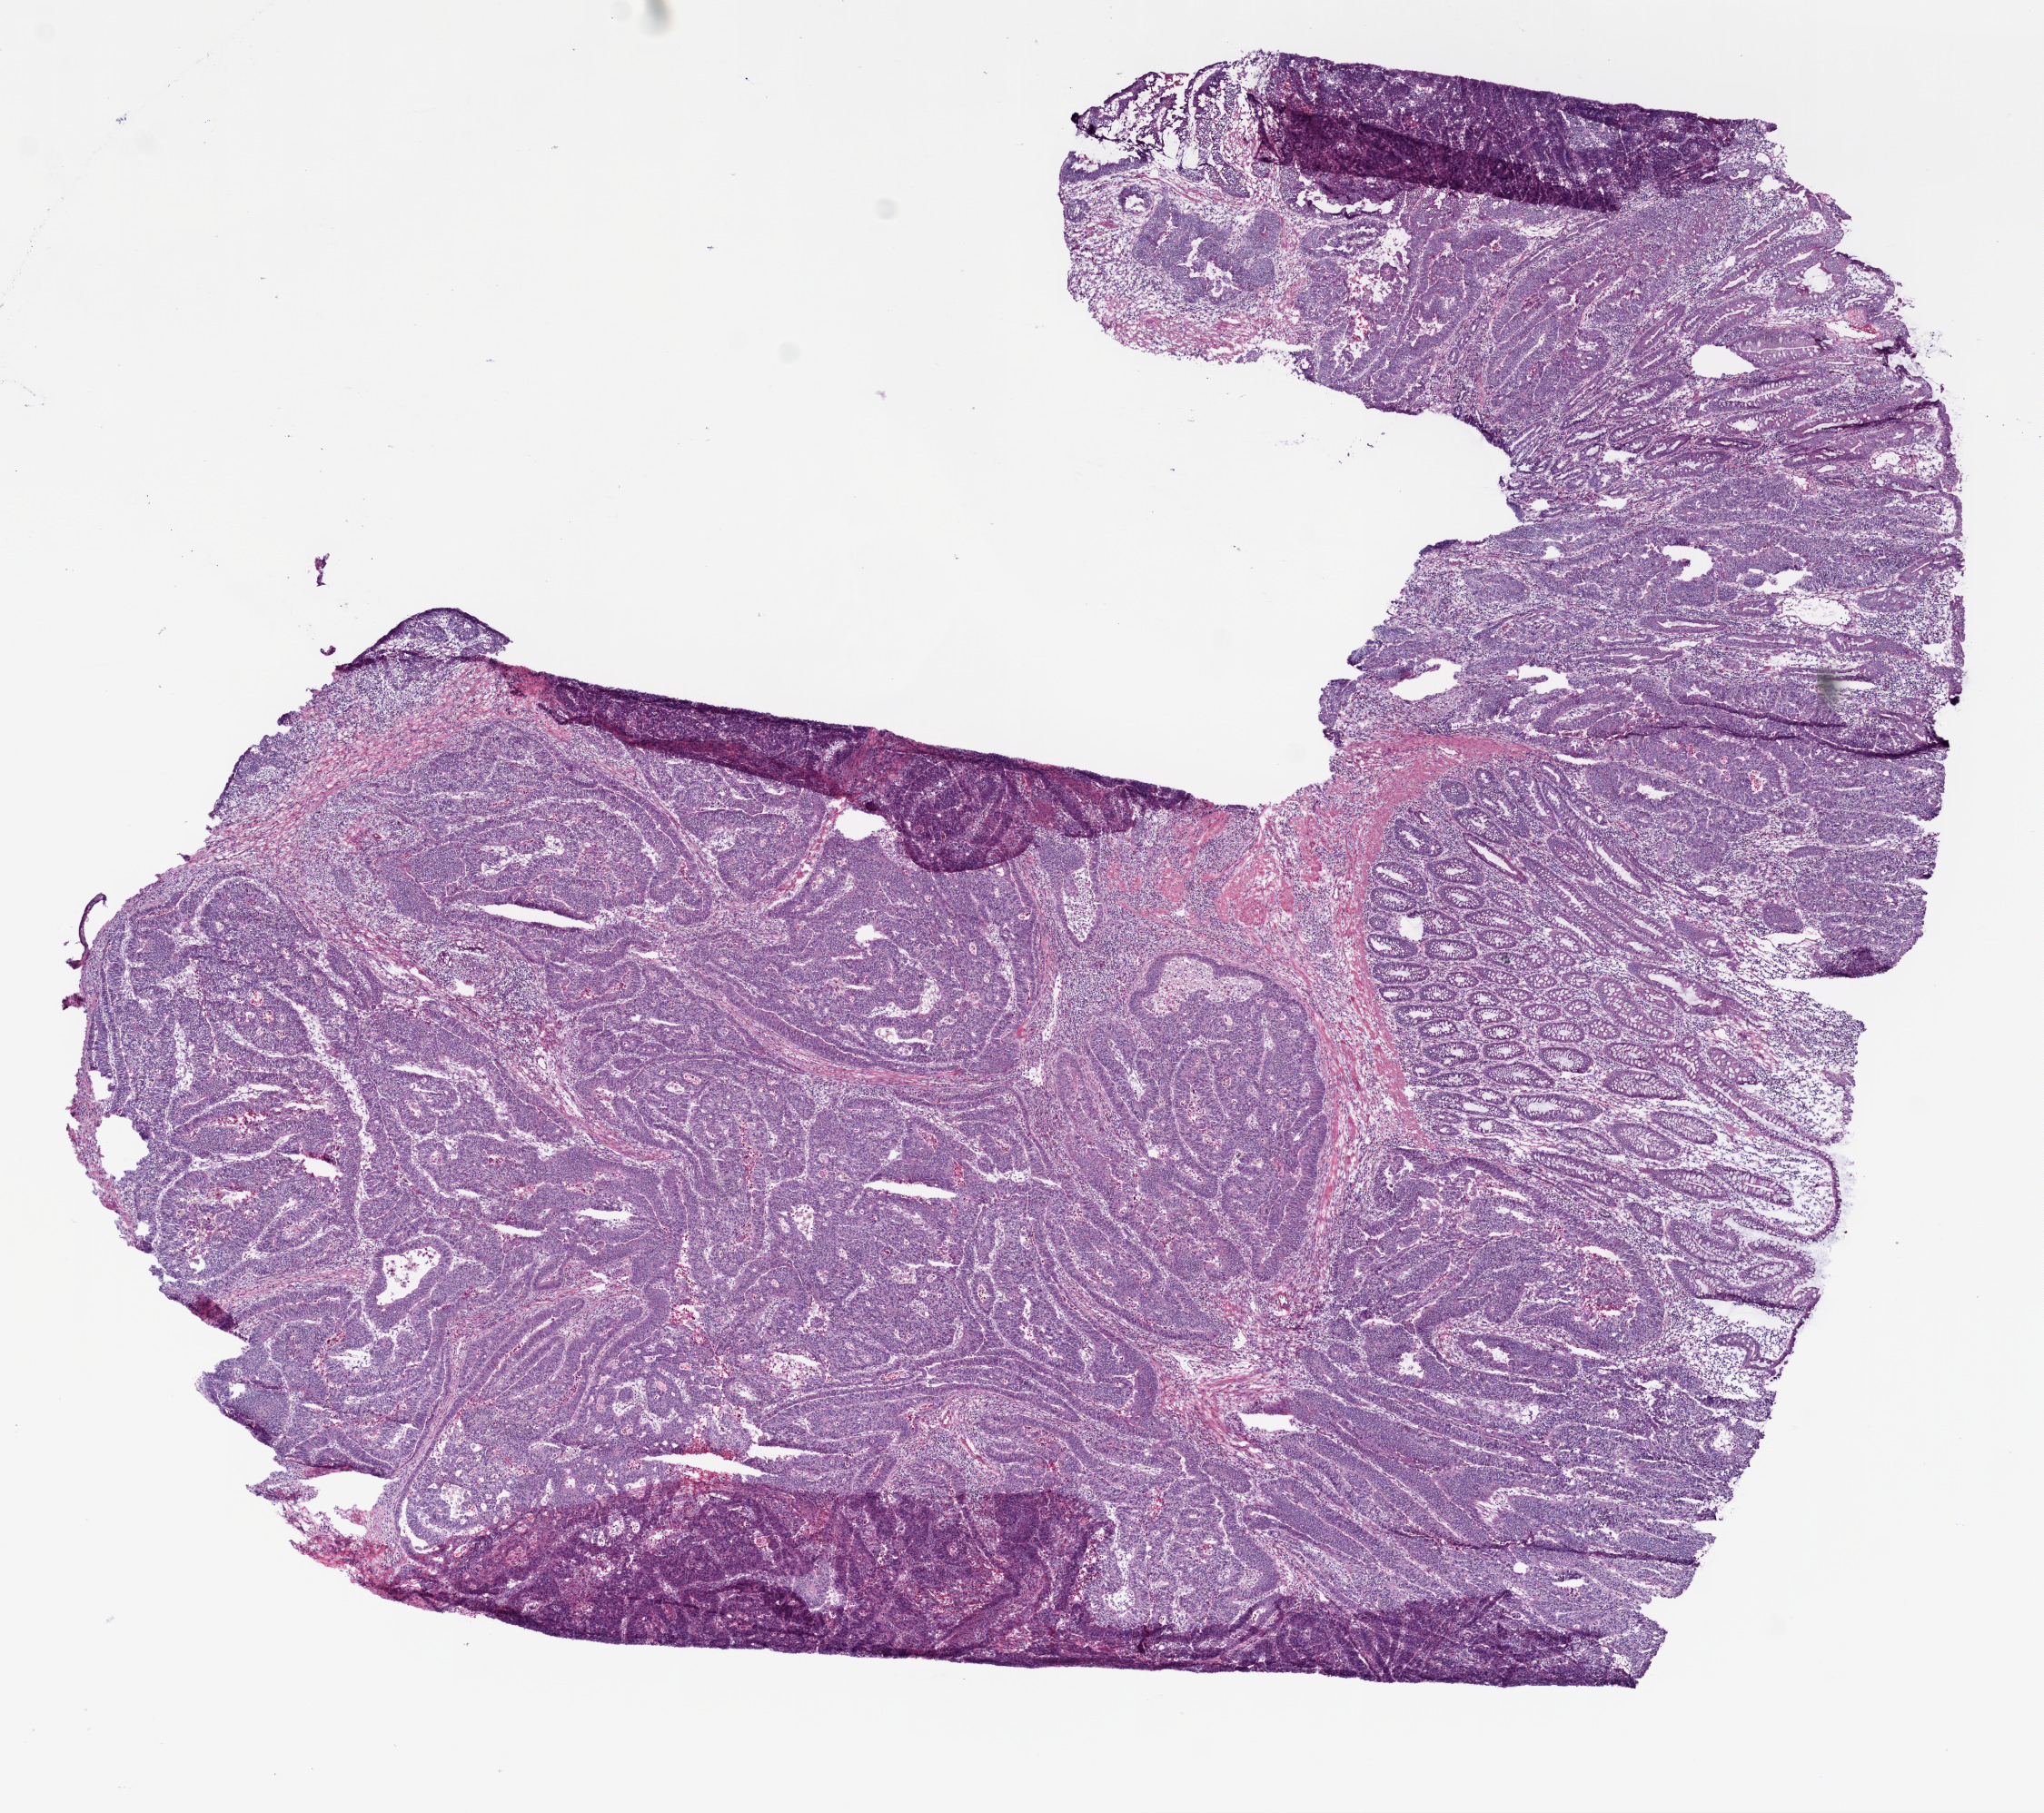
Hematoxylin and eosin (H&E) stained whole-slide image, whole scanned area (about 9.0 x 8.0 mm) shown as a low-resolution overview; frozen section from the bottom of the tissue portion; sample: primary tumour, rectum. Male, age 61 years at initial diagnosis. Composition of this section per pathologist review: tumour cells 67%, tumour nuclei 70%, normal cells 15%, stromal cells 10%, necrosis 8%.
* lymph nodes positive (case pathology): 0 of 17 examined
* pathologic diagnosis: Adenocarcinoma, NOS (rectosigmoid junction)
* AJCC pathologic stage: IIA (6th edition)